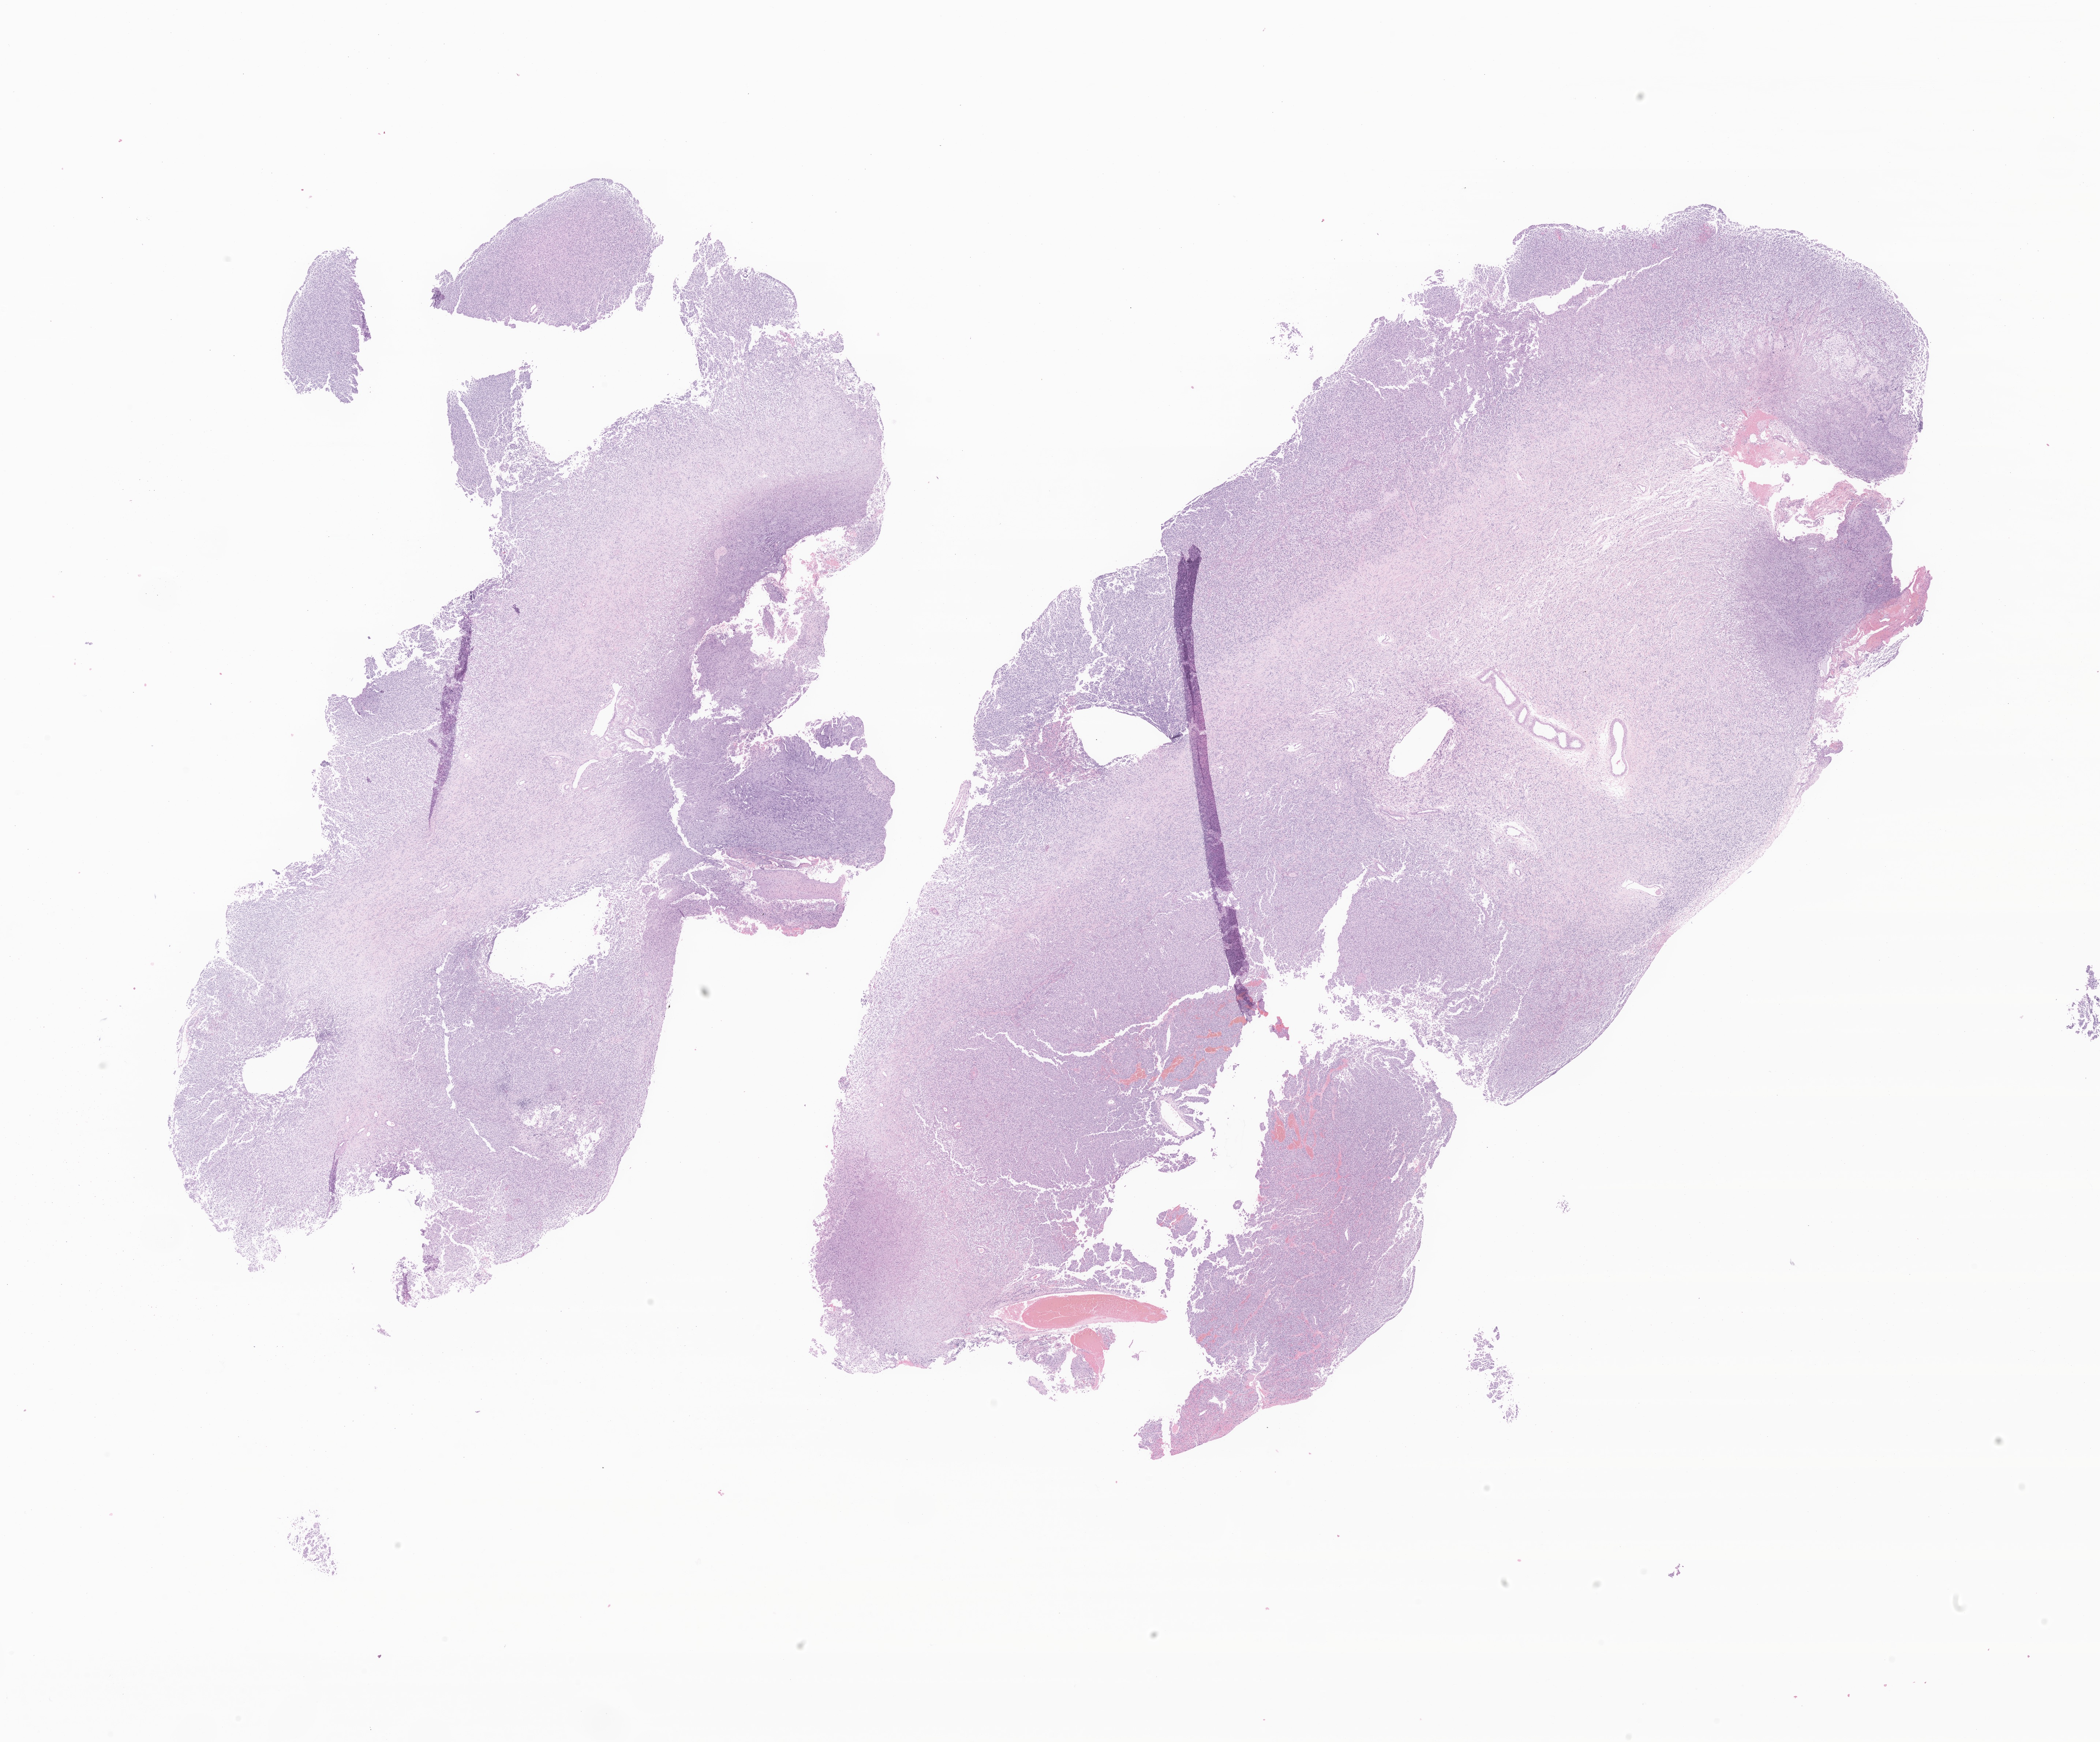
Whole-slide image, H&E stain of tumor tissue from the brain — a low-resolution overview of the entire scanned area, about 24.2 x 20.1 mm; formalin-fixed, paraffin-embedded (FFPE) tissue. Patient: male, age 111 days.
Recorded diagnosis: Glioma, malignant.